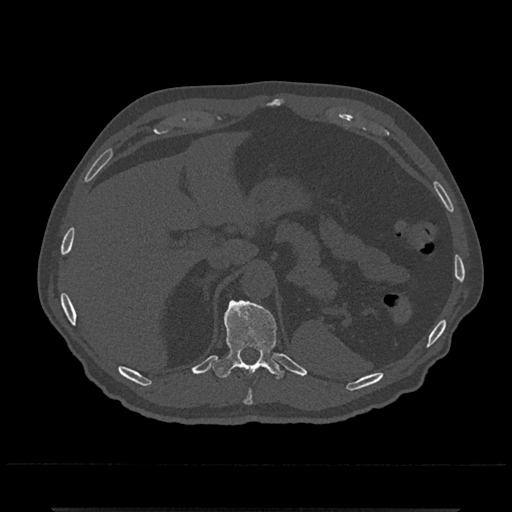
CT including the spine, one axial slice. Slice 504 of 797 in the series (ordered by position). Reconstruction kernel Br40s/3. 120 kVp. Bone window (W 1800 / L 400 HU). 512 × 512 image matrix, field of view 393 × 393 mm. Patient: male, 67 years. From the clinical record (not read from this slice): primary cancer: prostate.
Structures marked on this image (semi-automatic segmentation, software-assisted and operator-edited):
- T10 vertebra: box from (x=243, y=389) to (x=253, y=405) px
- T11 vertebra: (x=212, y=300)–(x=285, y=379)